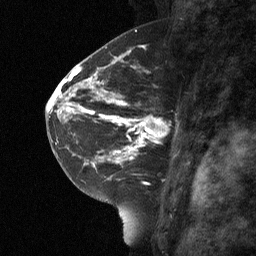
Breast MRI (dynamic contrast-enhanced), one sagittal slice. Slice 37 of 64 in the series (ordered by position). Dynamic contrast-enhanced study with each time point stored as its own series, time point 2 of 3 at this slice position (early post-contrast, ordered by acquisition time). 1.5 T. TE 4.8 ms, TR 27 ms. 2 mm slice thickness. 256 × 256 image matrix, field of view 180 × 180 mm. Female patient, age 42 years. Case-level facts recorded for this patient, not image findings: setting: breast cancer imaged before/during neoadjuvant chemotherapy; receptor status: triple-negative.
Annotated regions visible in this slice (semi-automatically segmented with operator editing):
- analysis volume of interest (the breast-tissue region the enhancement analysis was run in; not a lesion): bounding box <115,92,188,160> (left, top, right, bottom; pixels)
- tumour enhancement mask (voxels above the 90 % enhancement threshold inside the analysis volume of interest): <115,95,152,160>